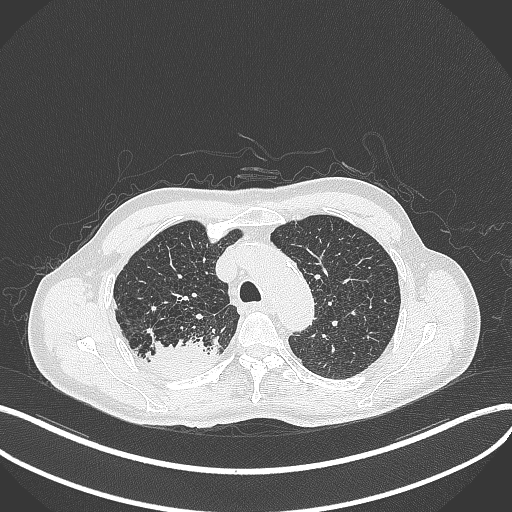
Chest CT, one axial slice; reconstruction kernel B70f; lung window (W 1500 / L -600 HU); 512 × 512 image matrix, field of view 400 × 400 mm. Patient: male, 79 years. From the clinical record (not read from this slice): clinical TNM (as recorded): T3 N0 M0.
Annotated regions visible in this slice (bounding box drawn by a radiologist):
- lung tumour (recorded histology: adenocarcinoma): bounding box [x1, y1, x2, y2] px = [138, 336, 224, 380]